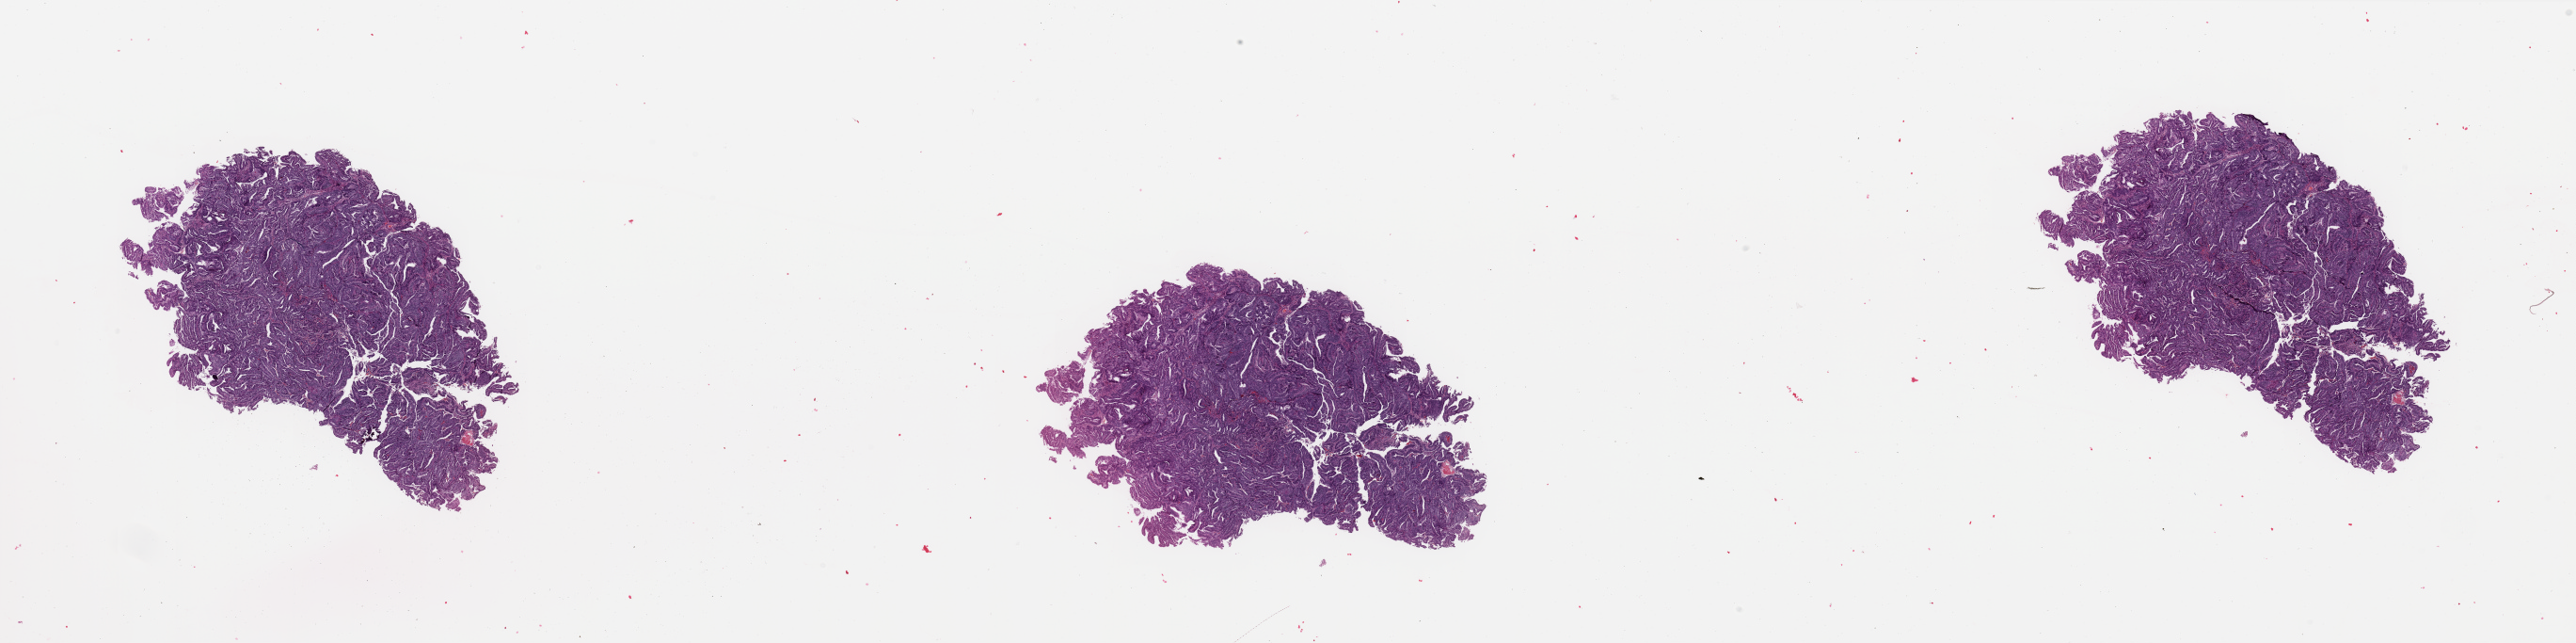
Whole-slide histology image, Hematoxylin and eosin (H&E) stained — a low-resolution overview of the entire scanned area, about 43.3 x 10.8 mm, tumour tissue sample, uterus. Patient: female, age 39 years. Histologic grade: G2 (moderately differentiated).
AJCC pathologic stage: I. Diagnosis: Endometrioid adenocarcinoma, NOS.